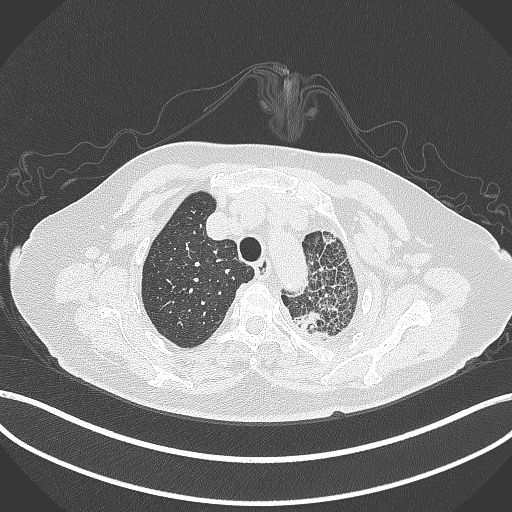
Chest CT, one axial slice; slice 322 of 399 in the series (ordered by position); 120 kVp; lung window (W 1500 / L -600 HU); 1 mm slice thickness; 512 × 512 image matrix, field of view 400 × 400 mm. Patient: female, 75 years. Case-level facts recorded for this patient, not image findings: clinical TNM (as recorded): T3 N3 M1.
Outlined on this slice (bounding box drawn by a radiologist):
- lung tumour (recorded histology: adenocarcinoma): bounding box <293,307,333,343> (left, top, right, bottom; pixels)